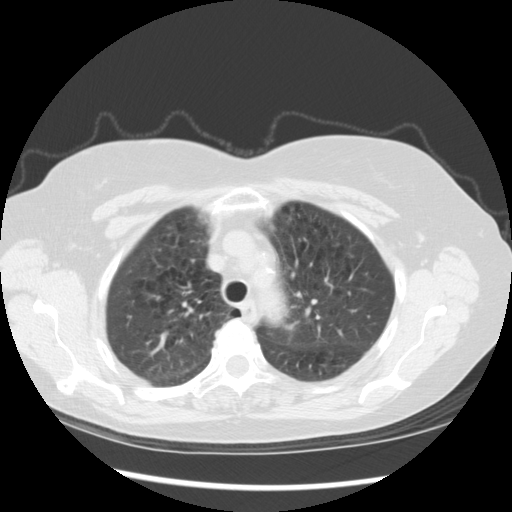
Low-dose screening chest CT, axial slice; baseline annual screen; lung window (W 1500 / L -600 HU); standard (soft-tissue) reconstruction kernel (STANDARD); 120 kVp; slice 99 of 123 in the series; 512 × 512 image matrix, field of view 360 × 360 mm. Female participant, aged 70 years at enrolment. Current smoker at enrolment.
Lesion marked by an expert reader, bounding box [x1, y1, x2, y2] px = [268, 306, 313, 350]. Screening reader's record for this exam: no non-calcified nodule ≥4 mm recorded. Lung cancer was diagnosed 757 days after this screen: neoplasm, malignant, left upper lobe, stage IIIB (AJCC 6th edition), 40 mm at pathology.